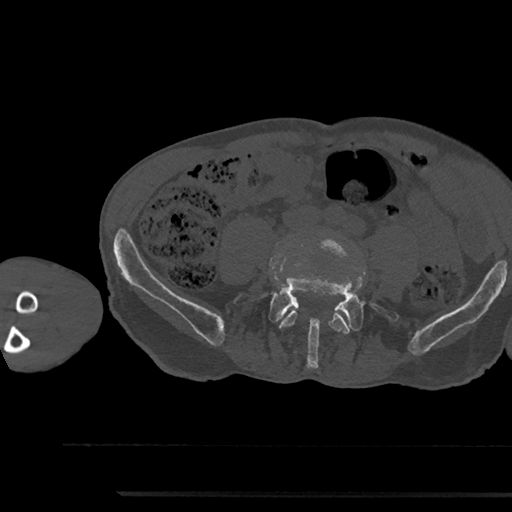
CT including the spine, one axial slice. Position 372 of 797 along the scan axis. Reconstruction kernel Br40s/3. 120 kVp. Bone window (W 1800 / L 400 HU). 0.5 mm slice thickness. 512 × 512 image matrix, field of view 367 × 367 mm. Male patient, age 79 years. Case-level facts recorded for this patient, not image findings: primary cancer: prostate.
Structures marked on this image (semi-automatic segmentation, software-assisted and operator-edited):
- L4 vertebra: bounding box [x1, y1, x2, y2] px = [279, 238, 351, 334]
- L5 vertebra: [234, 266, 399, 367]